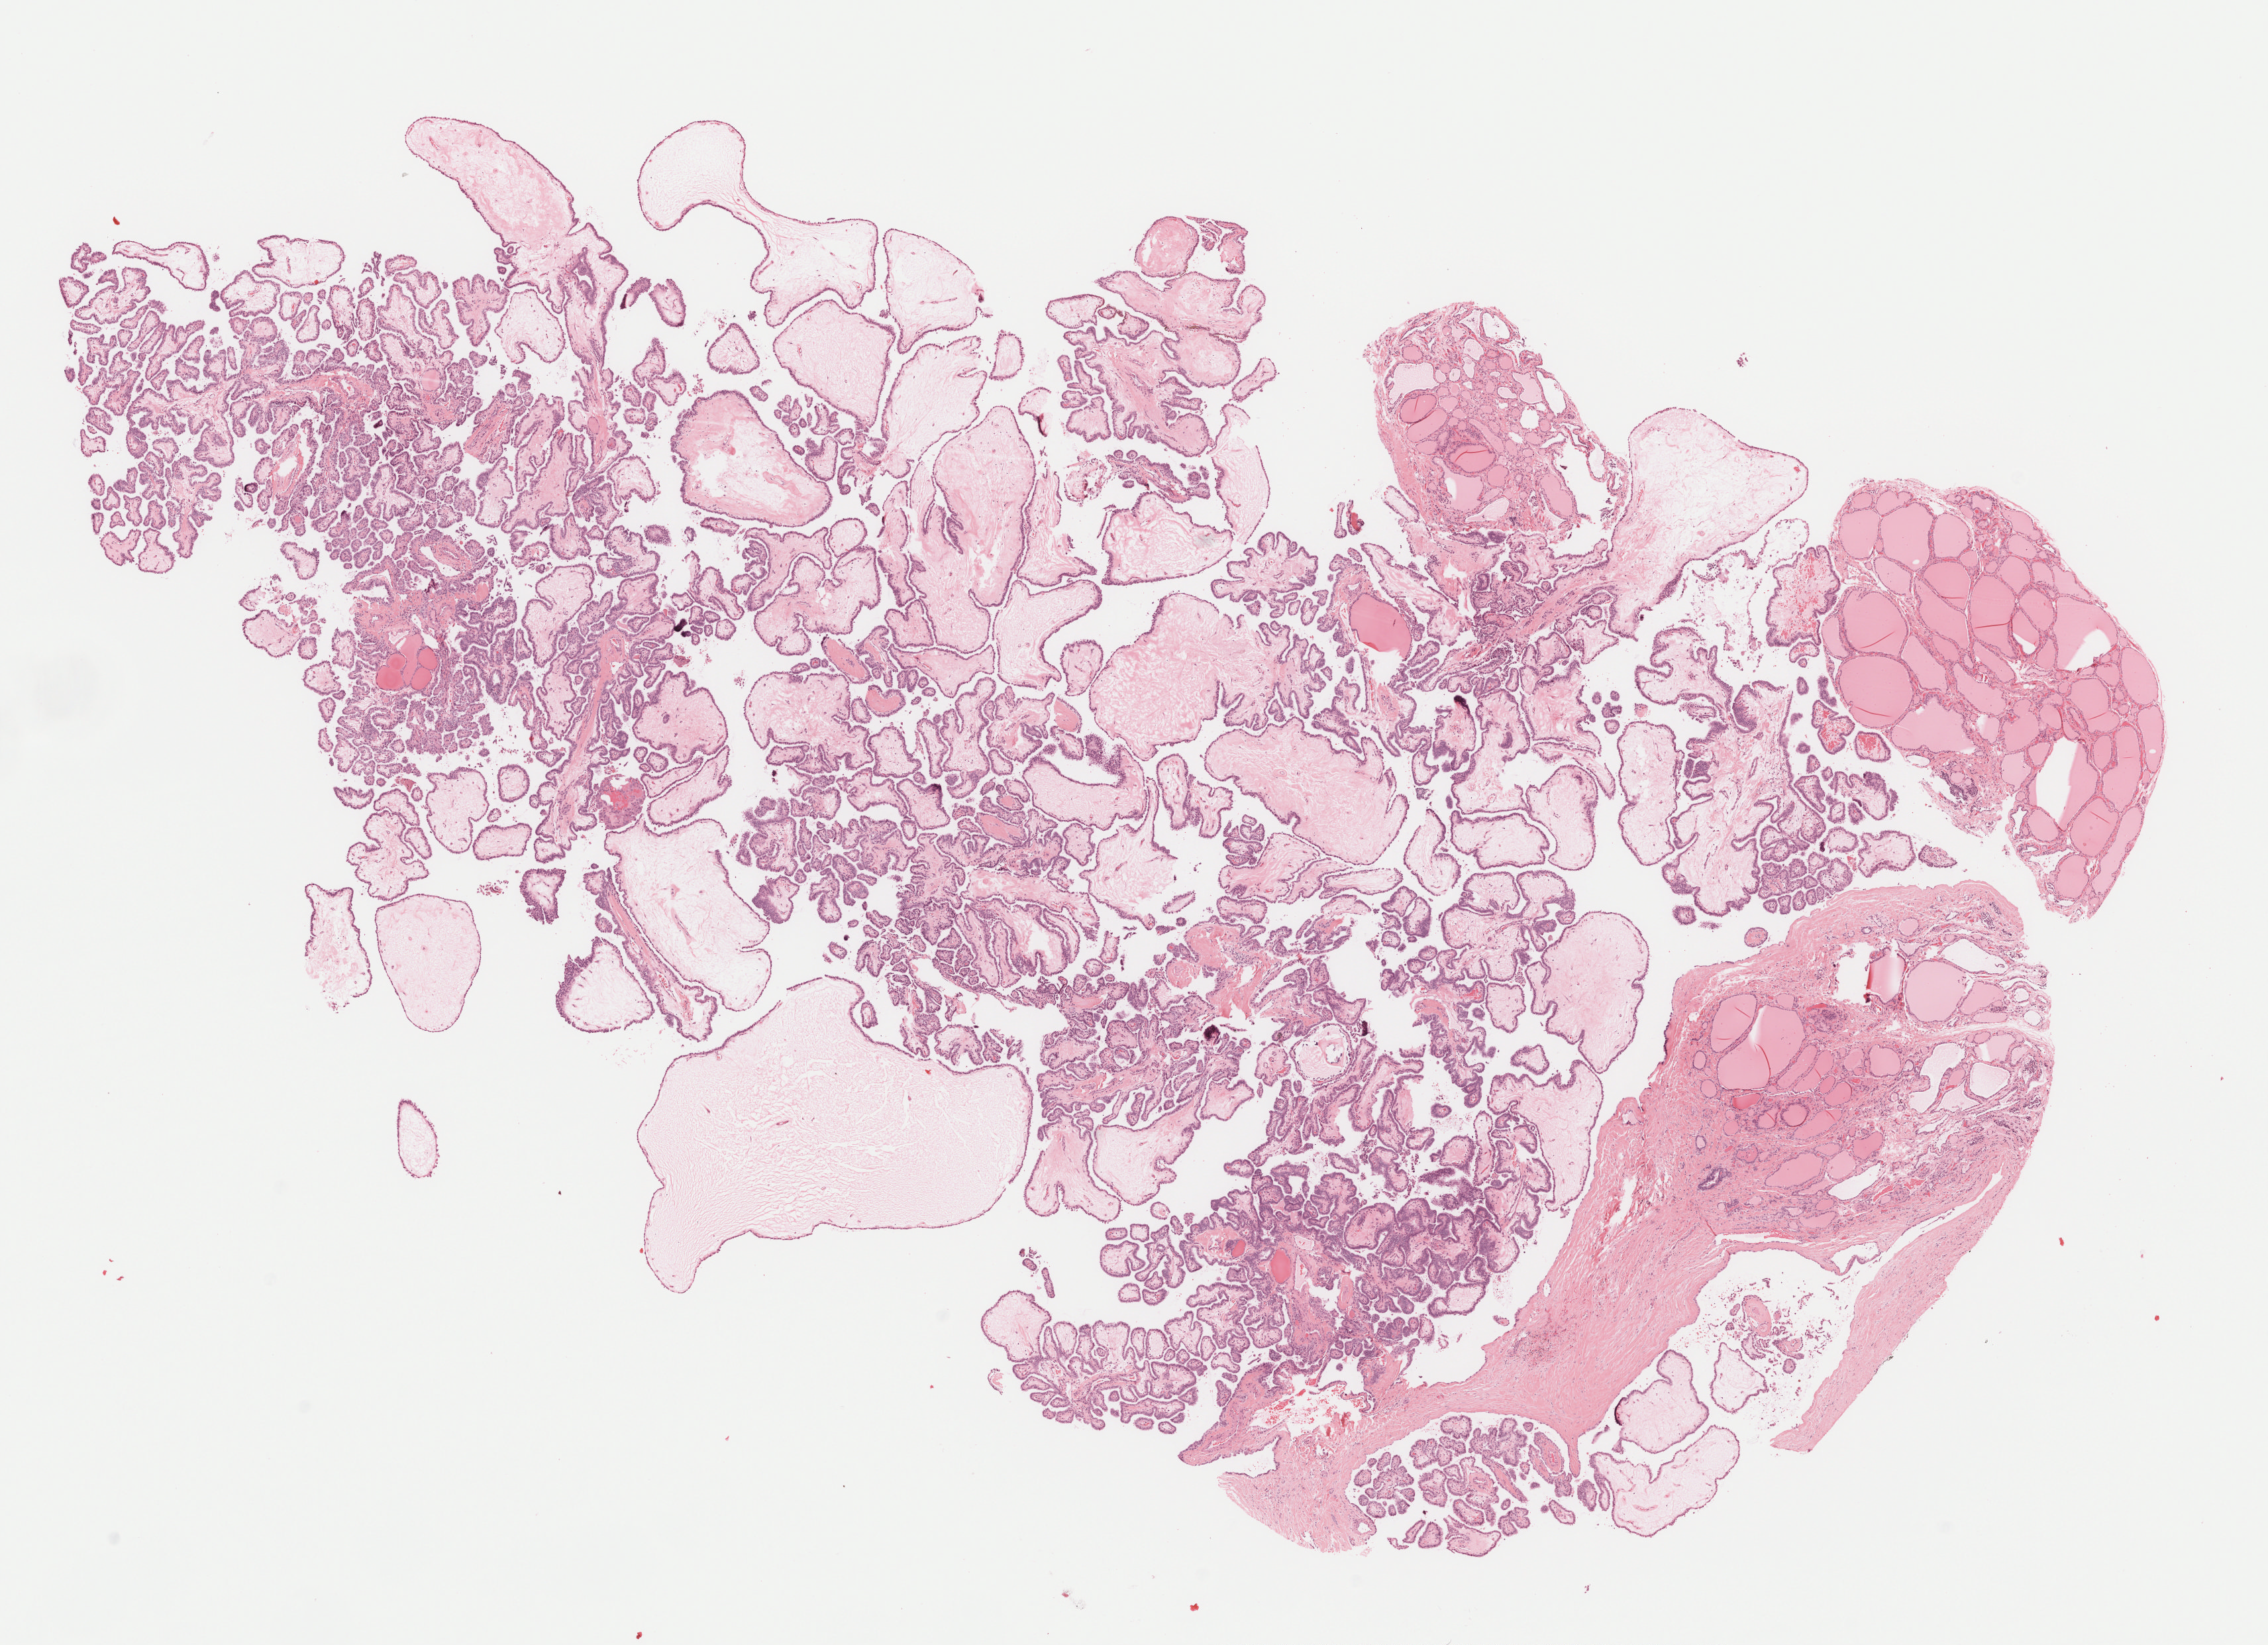
Digitized Hematoxylin and eosin (H&E) stained tissue section (whole slide), low-resolution overview of the scanned area, about 13.8 x 10.0 mm. Formalin-fixed paraffin-embedded (FFPE) diagnostic section. Sample: primary tumour, thyroid. Male patient; age at initial diagnosis 33 years.
- histologic diagnosis: Papillary adenocarcinoma, NOS (thyroid gland)
- lymph nodes positive (case pathology): 9 of 34 examined
- AJCC pathologic stage: I (7th edition)